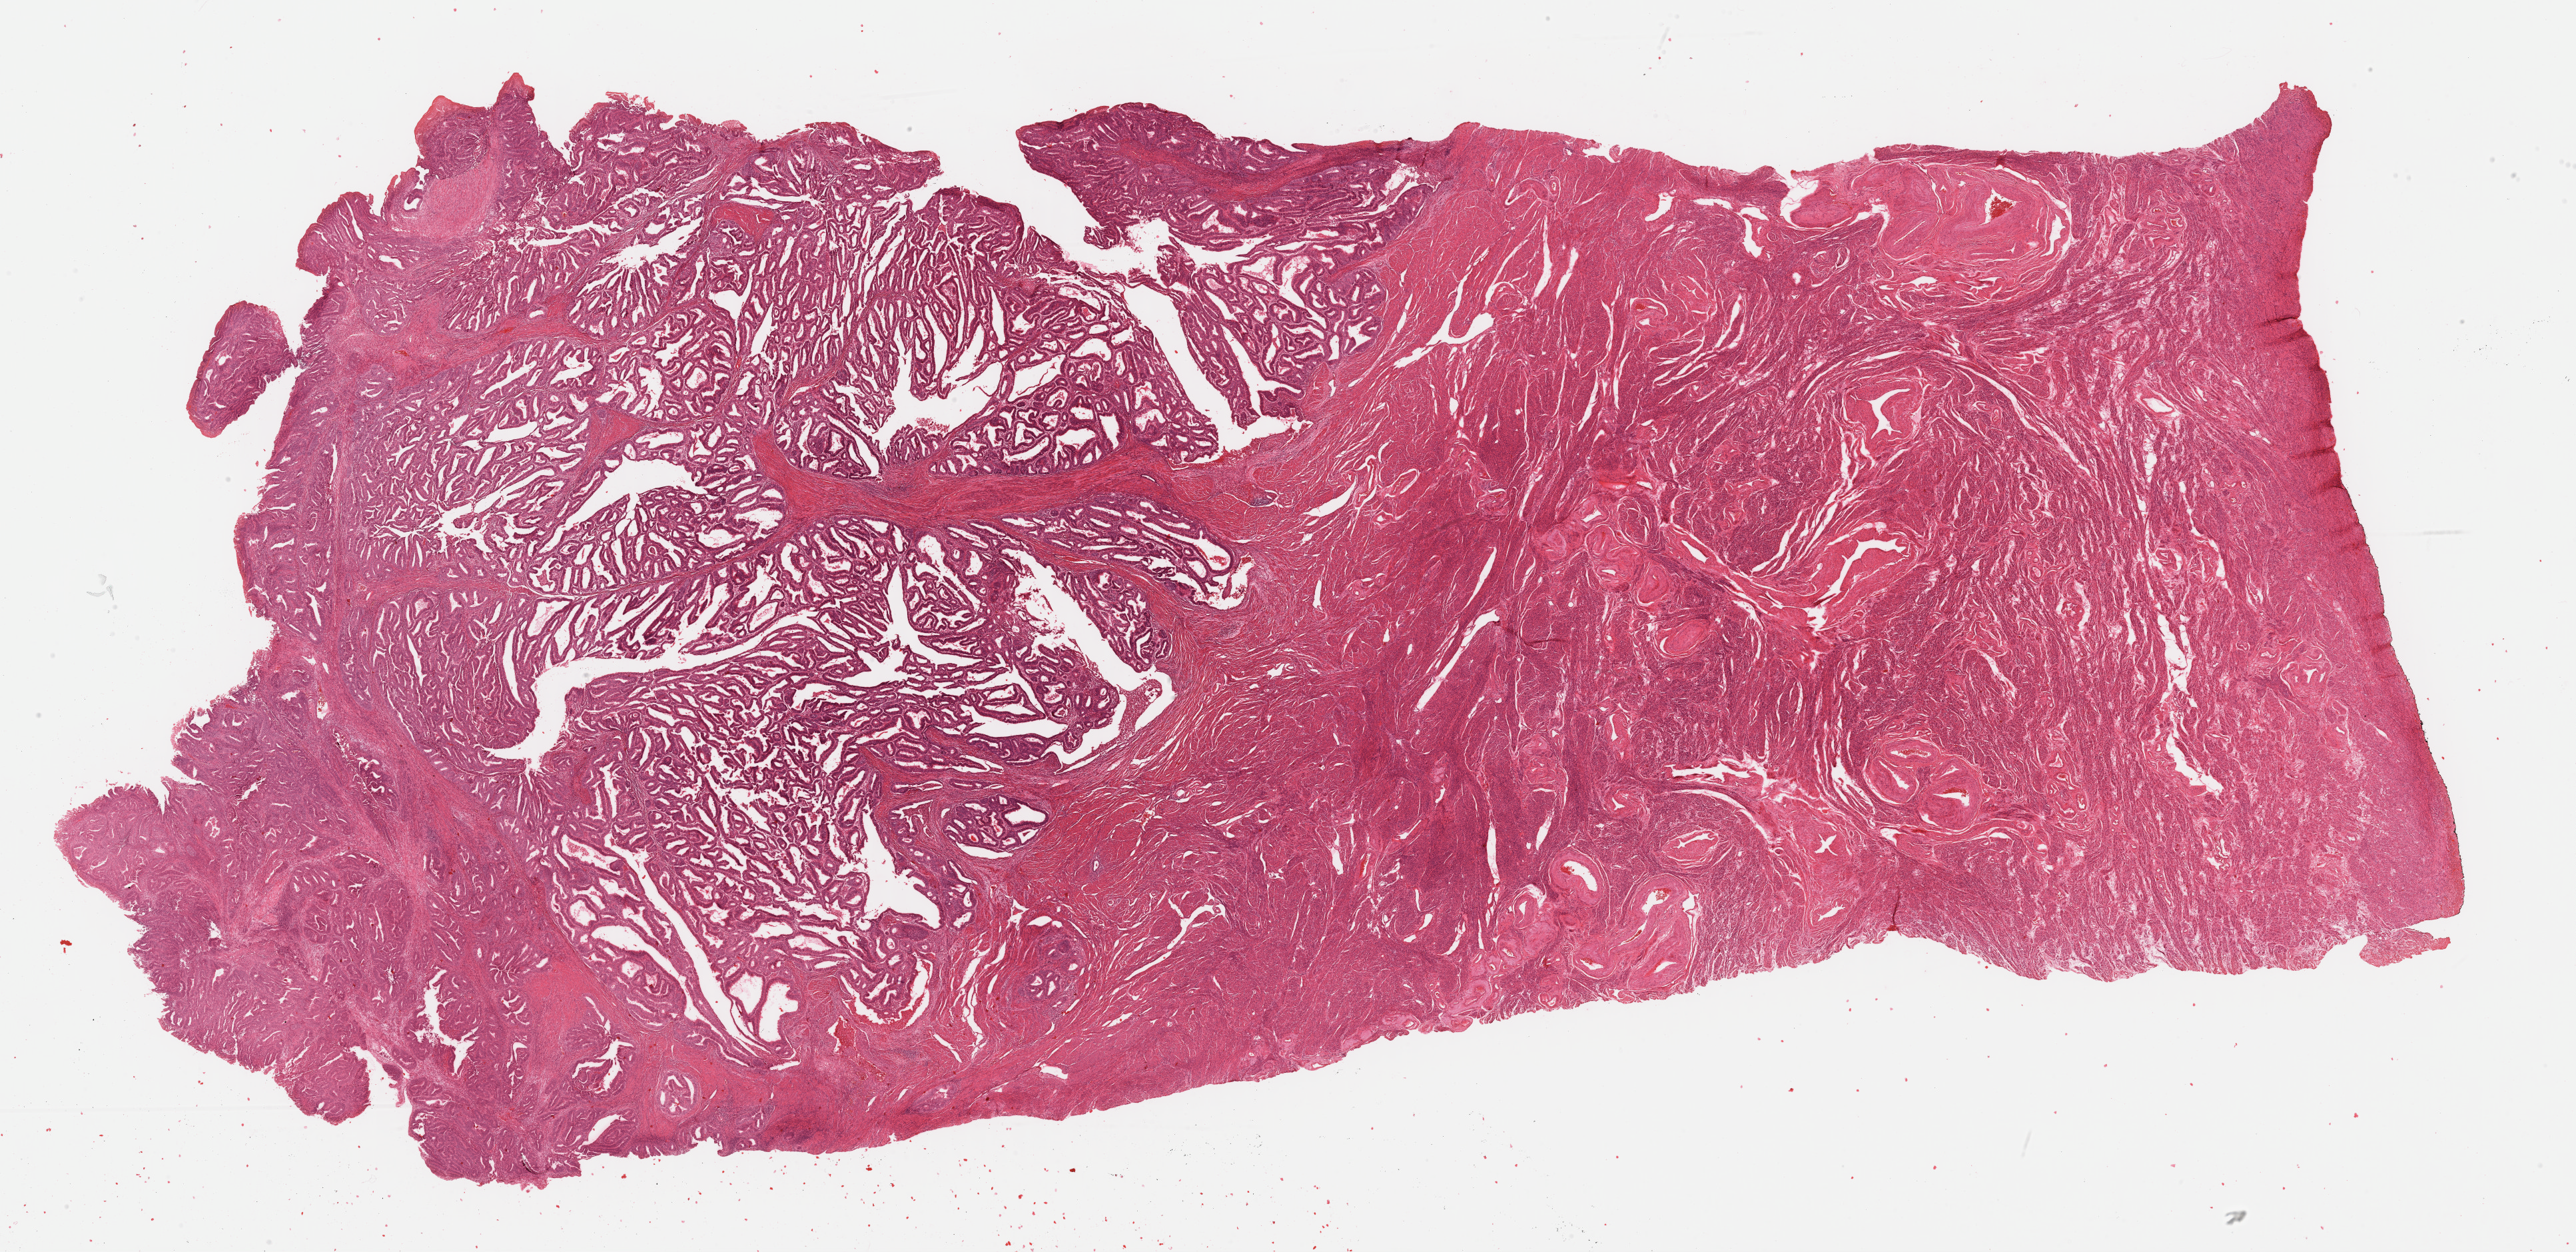
Whole-slide histology image, Hematoxylin and eosin (H&E) stained — low-resolution overview of the scanned area, about 30.5 x 14.8 mm (slide scanned at 40x), formalin-fixed paraffin-embedded (FFPE) diagnostic section, primary tumour sample from the uterus. Female patient; age at initial diagnosis 63 years. Histologic grade: G1 (well differentiated).
Histologic diagnosis: Endometrioid adenocarcinoma, NOS (endometrium). FIGO stage: IB.